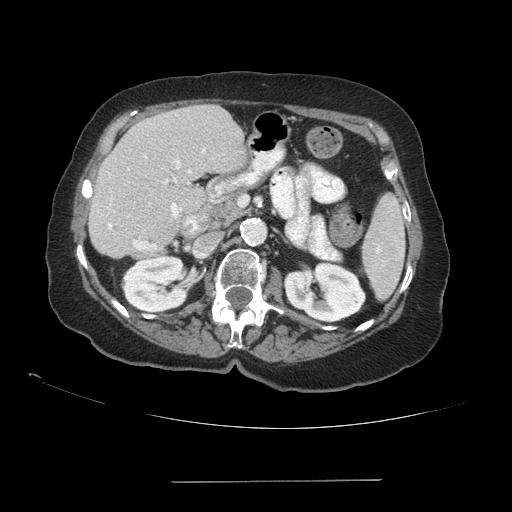
Contrast-enhanced abdominal CT (liver protocol), one axial slice; slice 46 of 89 in the series (ordered by position); reconstruction kernel STANDARD; soft-tissue window (W 400 / L 40 HU); 2.5 mm slice thickness; 512 × 512 image matrix. From the clinical record (not read from this slice): diagnosis: hepatocellular carcinoma (patient treated with transarterial chemoembolisation; whether this scan precedes or follows treatment is not stated here); TNM stage (as recorded): Stage-IVA; Child-Pugh class: A; tumour nodularity: uninodular.
Annotated regions visible in this slice (semi-automatic segmentation, software-assisted and operator-edited):
- liver parenchyma outside the tumour (the mass and vessels are separate outlines, so this box may not span the whole liver): bounding box (x1, y1, x2, y2) in pixels: (88, 104, 246, 258)
- liver vessels: (108, 148, 205, 250)